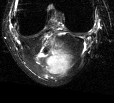
MRI of an extremity soft-tissue mass, one axial slice. Slice 12 of 44 in the series (ordered by position). T2-weighted fat-saturated. MR volume resampled by the dataset authors to the PET/CT grid (not the native acquisition matrix). 3.27 mm slice thickness. 114 × 103 image matrix, field of view 111 × 101 mm. Female patient. From the clinical record (not read from this slice): histological type: liposarcoma; site of the primary tumour: right thigh.
Outlined on this slice (expert contour drawn on MRI and transferred to this co-registered scan by the dataset authors):
- gross tumour volume (mass): bounding box [x1, y1, x2, y2] px = [34, 46, 73, 76]